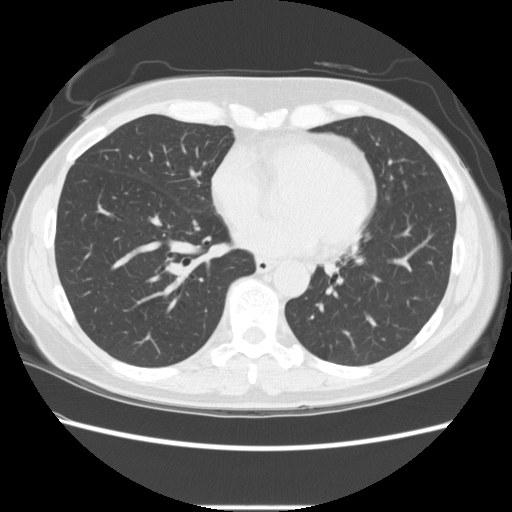
Chest CT (low-dose screening protocol), one axial image; first (baseline) screen; lung window (W 1500 / L -600 HU); slice 148 of 256 in the series; 512 × 512 image matrix. Female, age 60 years at enrolment.
- Expert-annotated lung lesion, bounding box [x1, y1, x2, y2] px = [392, 175, 418, 201].
- Screening reader's record for this exam: no non-calcified nodule ≥4 mm recorded.